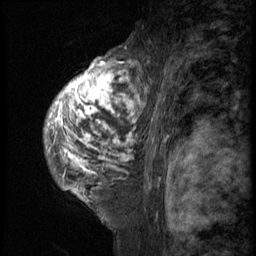
Breast MRI (dynamic contrast-enhanced), one sagittal slice; slice 40 of 58 in the series (ordered by position); 3 images stored at this slice position (order not interpretable as contrast timing); 1.5 T; TE 4.2 ms, TR 9 ms; 256 × 256 image matrix, field of view 180 × 180 mm. Female patient, age 50 years. Case-level facts recorded for this patient, not image findings: setting: breast cancer imaged before/during neoadjuvant chemotherapy; receptor status: triple-negative.
Annotated regions visible in this slice (semi-automatic segmentation, software-assisted and operator-edited):
- analysis volume of interest (the breast-tissue region the enhancement analysis was run in; not a lesion): box from (x=44, y=48) to (x=132, y=214) px
- tumour enhancement mask (voxels above the 140 % enhancement threshold inside the analysis volume of interest): (x=46, y=59)–(x=132, y=198)